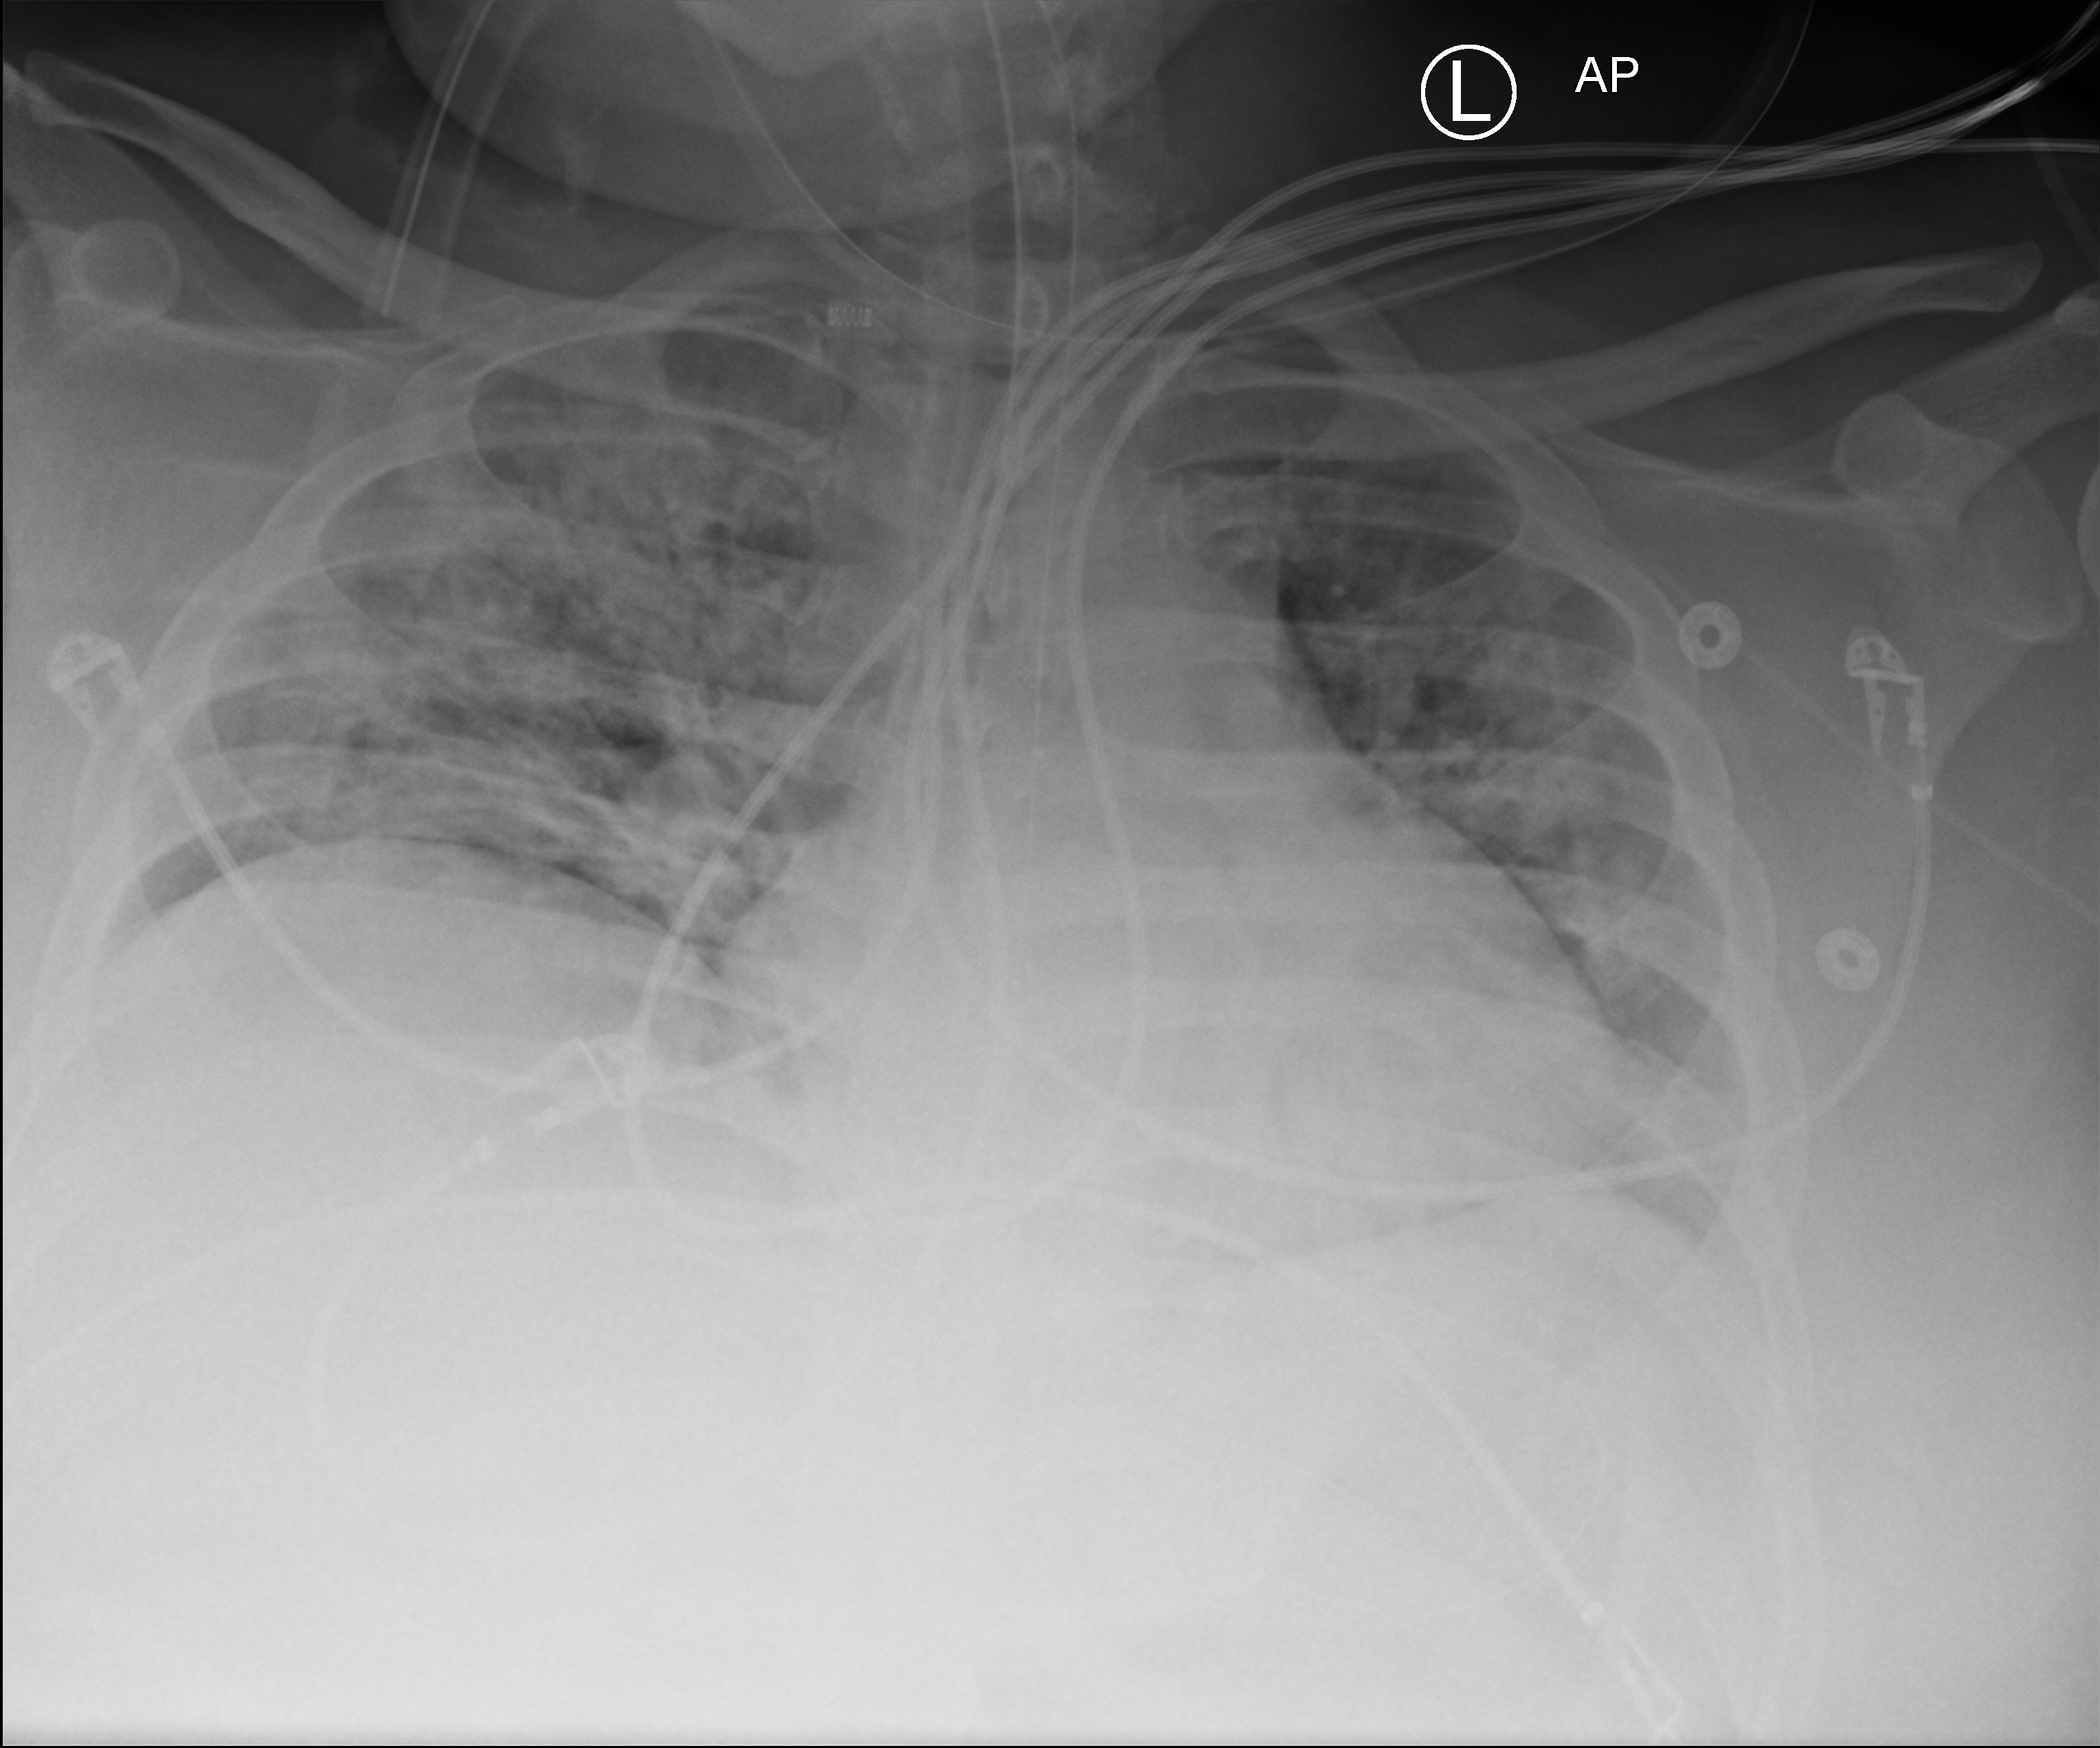
Portable chest radiograph, anteroposterior (AP) projection. Male patient hospitalised with COVID-19, age 18–59 years.
From the hospital-stay record, not from the radiograph (when in the stay this image was taken is not recorded):
- admitted to intensive care during this hospital stay: yes